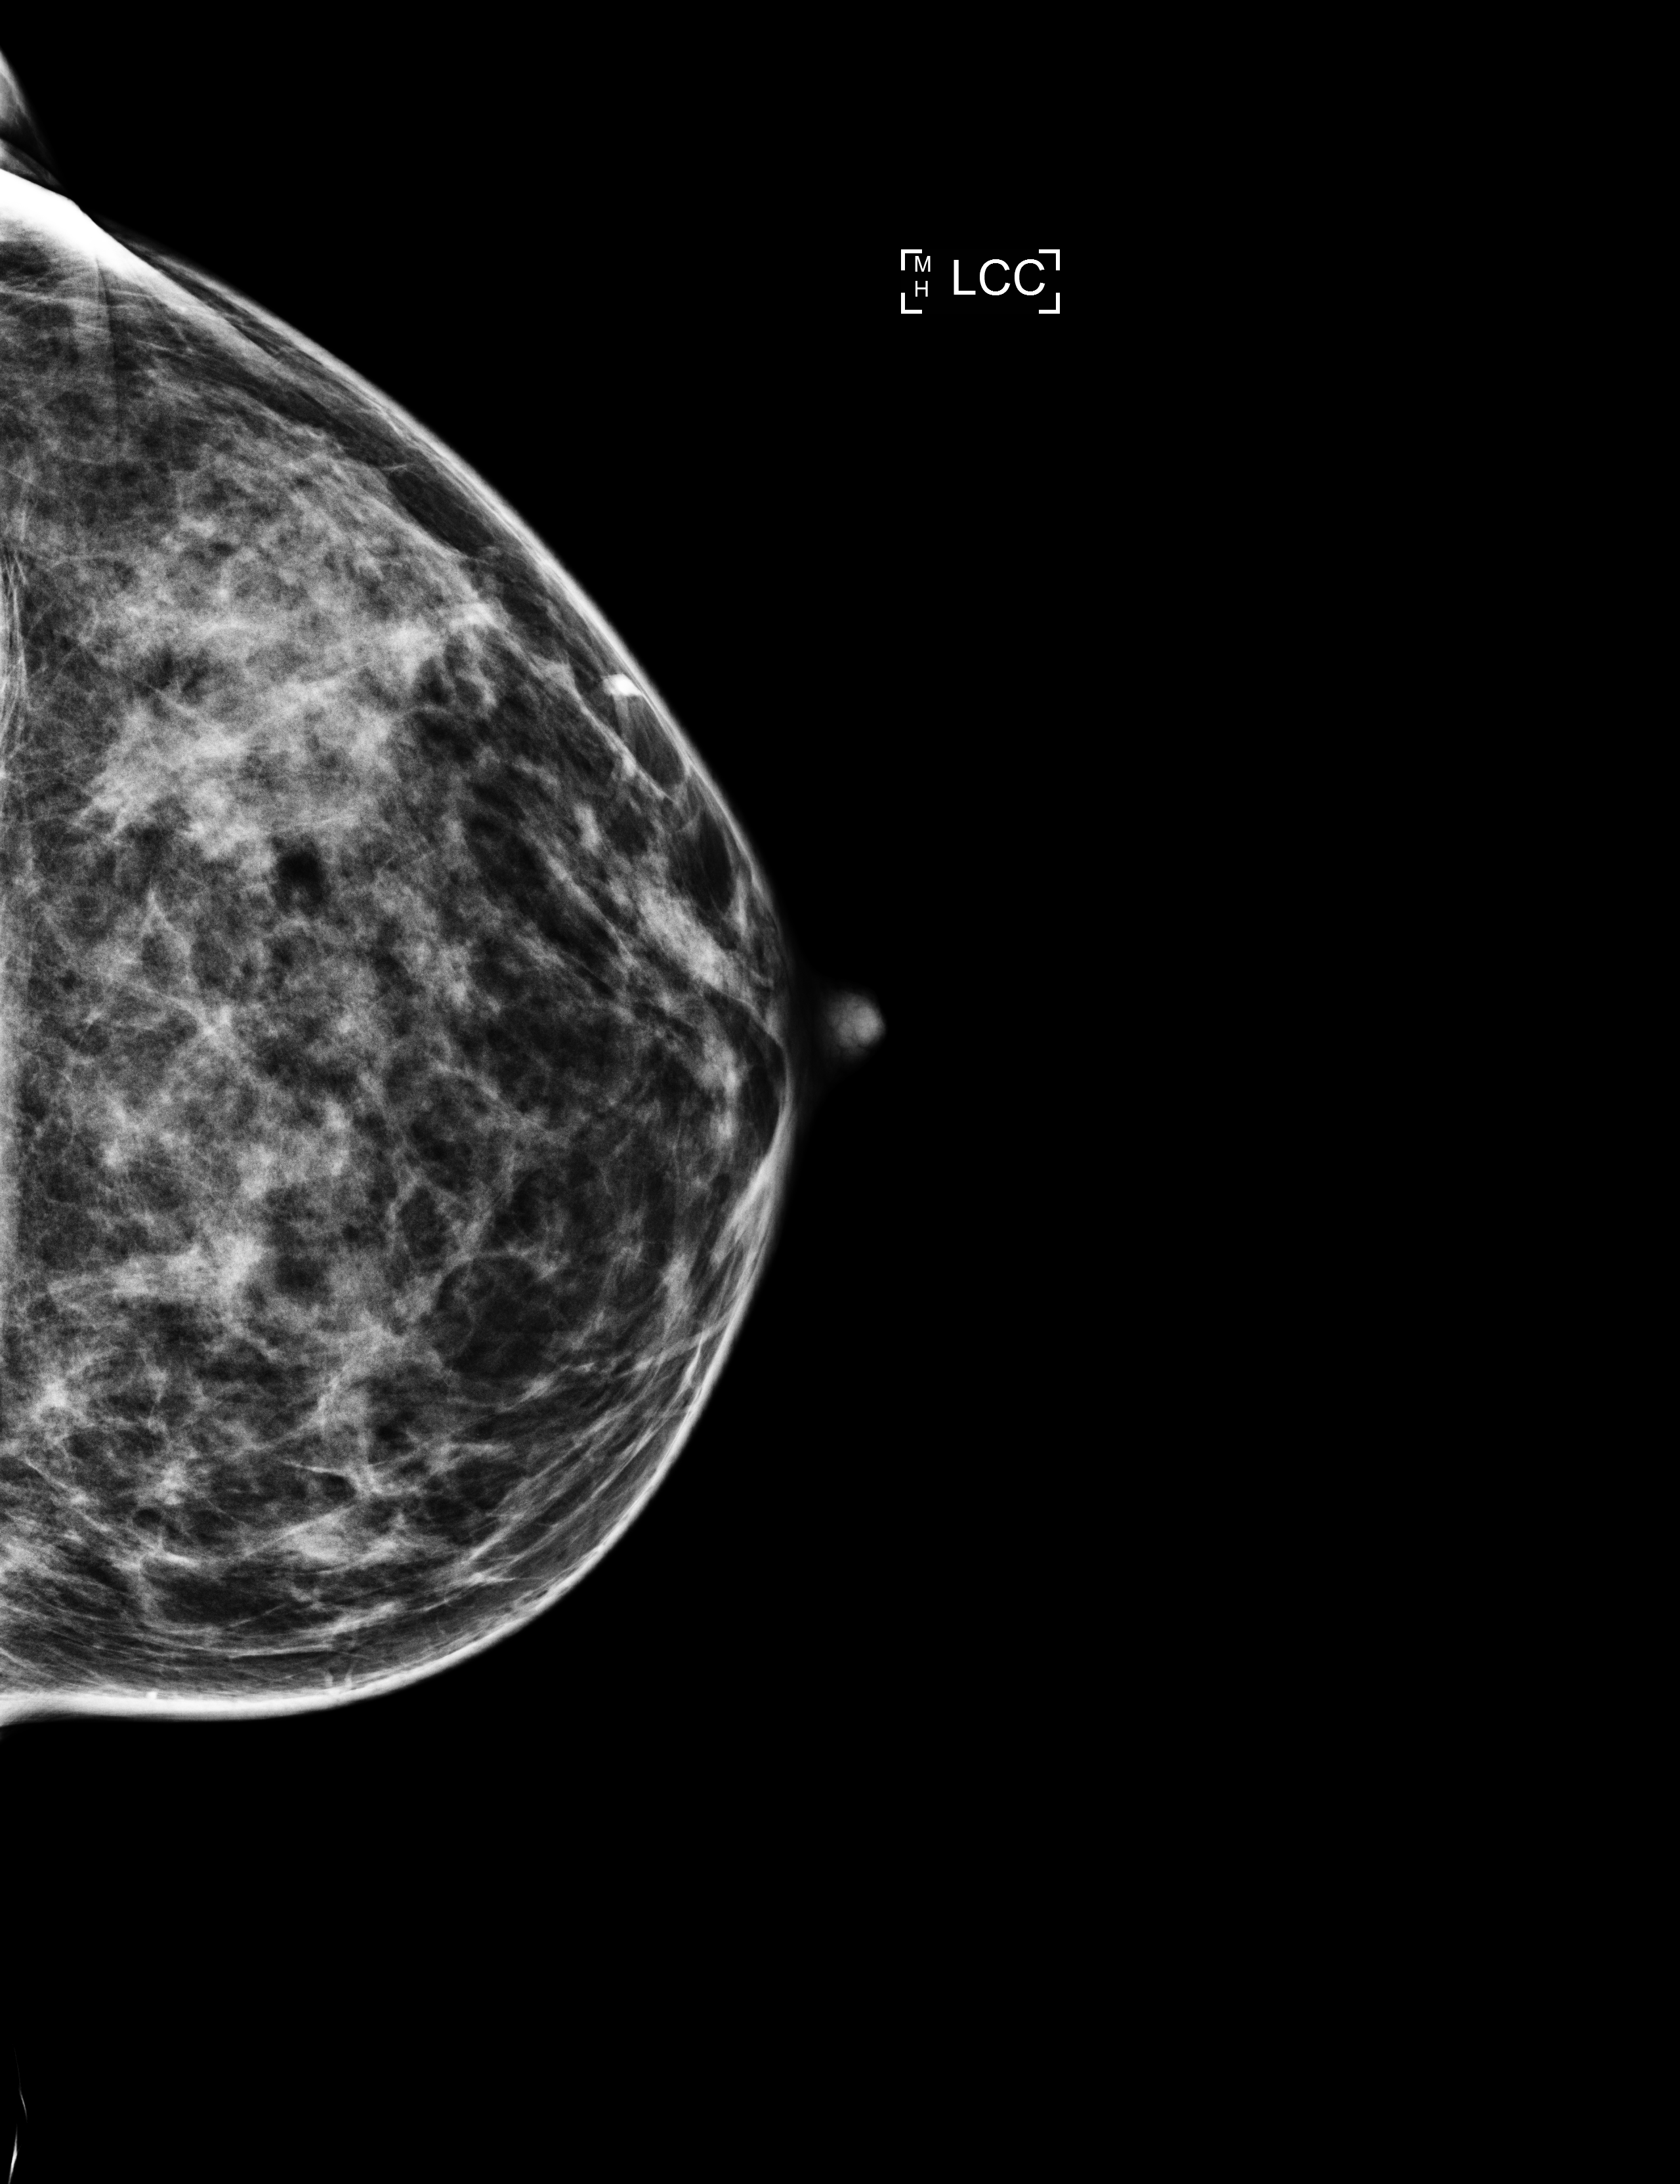
Annual screening mammography examination, compressed breast thickness 53 mm, system: Selenia Dimensions. Patient aged 42 years (female).
Image type: full-field digital mammogram. Breast: left. Projection: CC view.